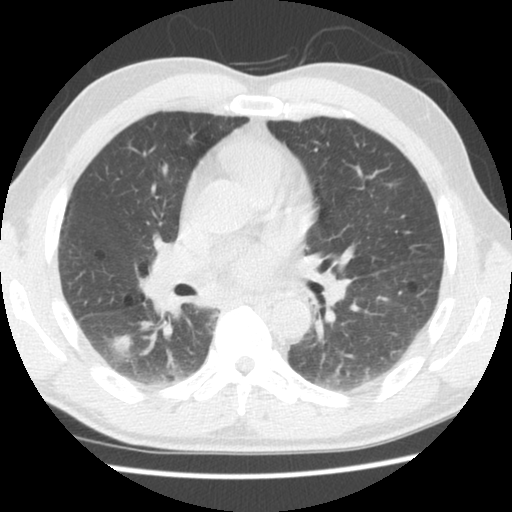
Chest CT (low-dose screening protocol), one axial image; second annual screen; lung window (W 1500 / L -600 HU); 2.5 mm slice thickness; standard (soft-tissue) reconstruction kernel (STANDARD); 512 × 512 image matrix, field of view 320 × 320 mm. Male, age 60 years at enrolment. Former smoker at enrolment.
Expert reader's lesion annotation, bounding box <89,318,145,372> (left, top, right, bottom; pixels). The exam's reader record, not a measurement of the box and not confirmed to be the same lesion: non-calcified nodule or mass ≥4 mm, right lower lobe, 17 × 15 mm, poorly defined margins, soft tissue attenuation, pre-existing on the prior screen: yes; interval growth: yes. Participant outcome: lung cancer diagnosed 44 days after this screen — adenocarcinoma, NOS, right lower lobe, stage IA (AJCC 6th edition), 18 mm at pathology.